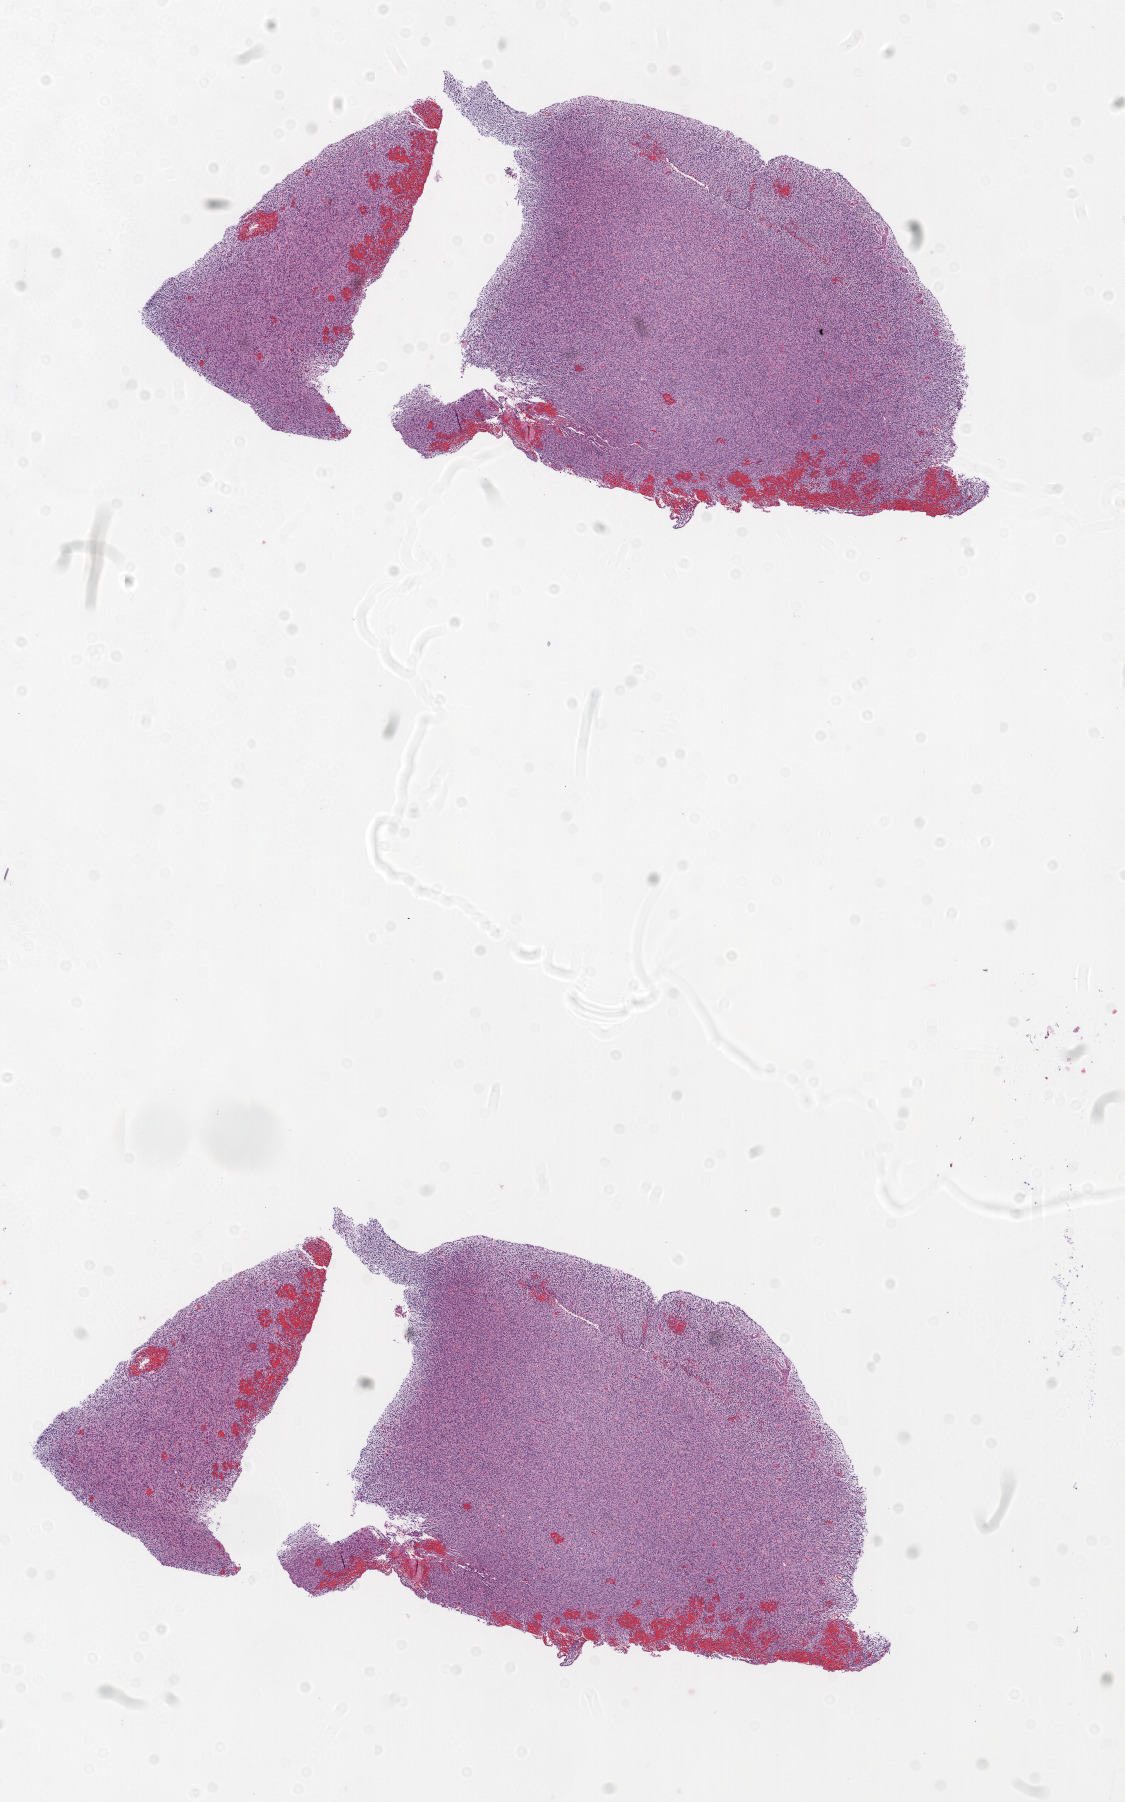
Digitized Hematoxylin and eosin (H&E) stained tissue section (whole slide), shown as a low-resolution overview of the whole scanned area (about 9.0 x 14.5 mm, slide scanned at 20x). Formalin-fixed paraffin-embedded (FFPE) diagnostic section. Primary tumour sample from the brain. Male patient; age at initial diagnosis 74 years.
Diagnosis: Glioblastoma.